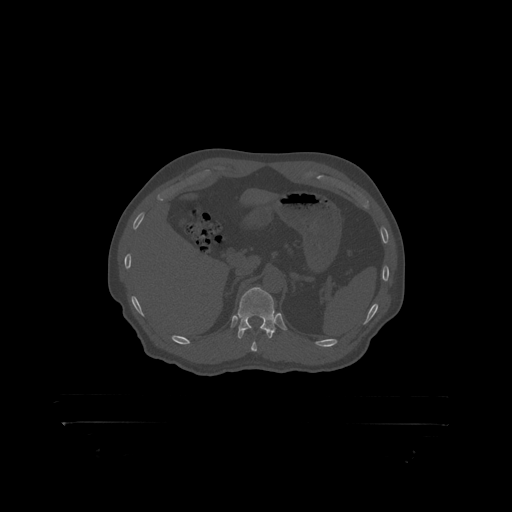
CT including the spine, one axial slice. Slice 361 of 399 in the series (ordered by position). Reconstruction kernel STANDARD. 120 kVp. Bone window (W 1800 / L 400 HU). 1.25 mm slice thickness. 512 × 512 image matrix. Male patient, age 46 years. Case-level facts recorded for this patient, not image findings: primary cancer: skin.
Structures marked on this image (semi-automatic segmentation, software-assisted and operator-edited):
- T12 vertebra: bounding box (x1, y1, x2, y2) in pixels: (238, 288, 280, 319)